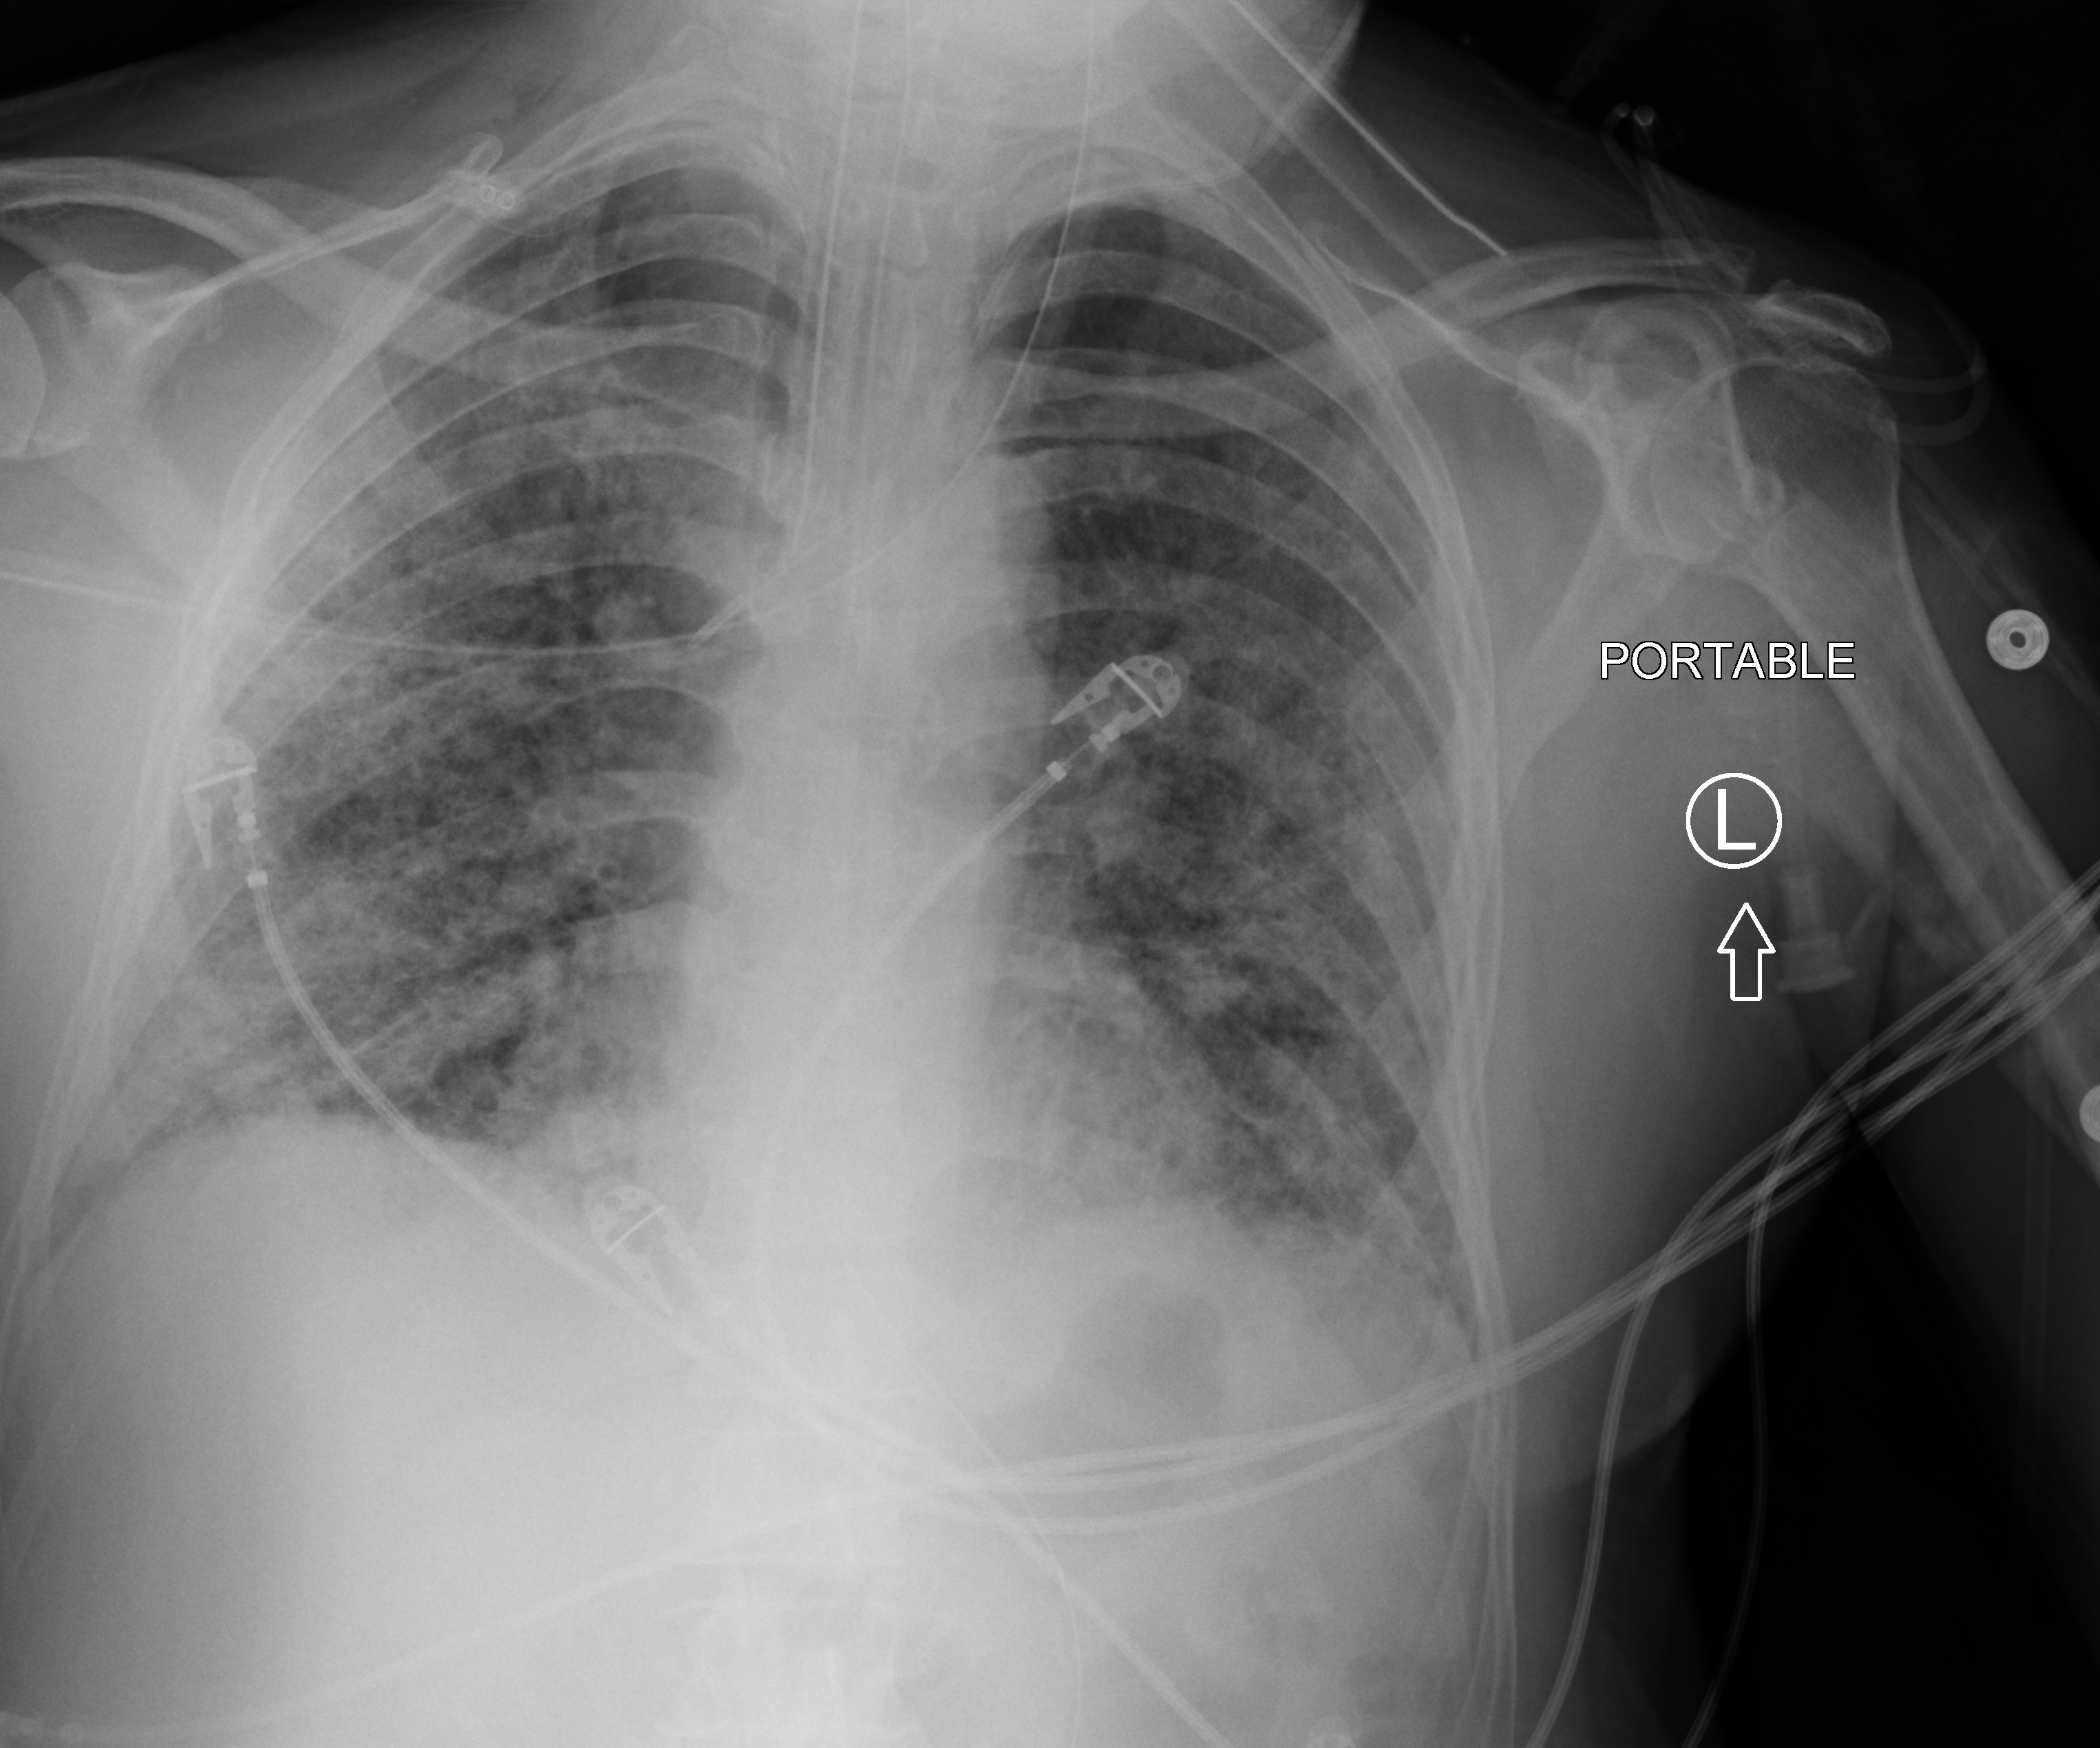
Portable chest radiograph; anteroposterior (AP) projection. Patient hospitalised with COVID-19; male, aged 60–74 years.
Admission-level facts for this patient (not findings on this image; timing relative to this image not recorded):
- smoking status (admission record): never
- admitted to intensive care during this hospital stay: yes